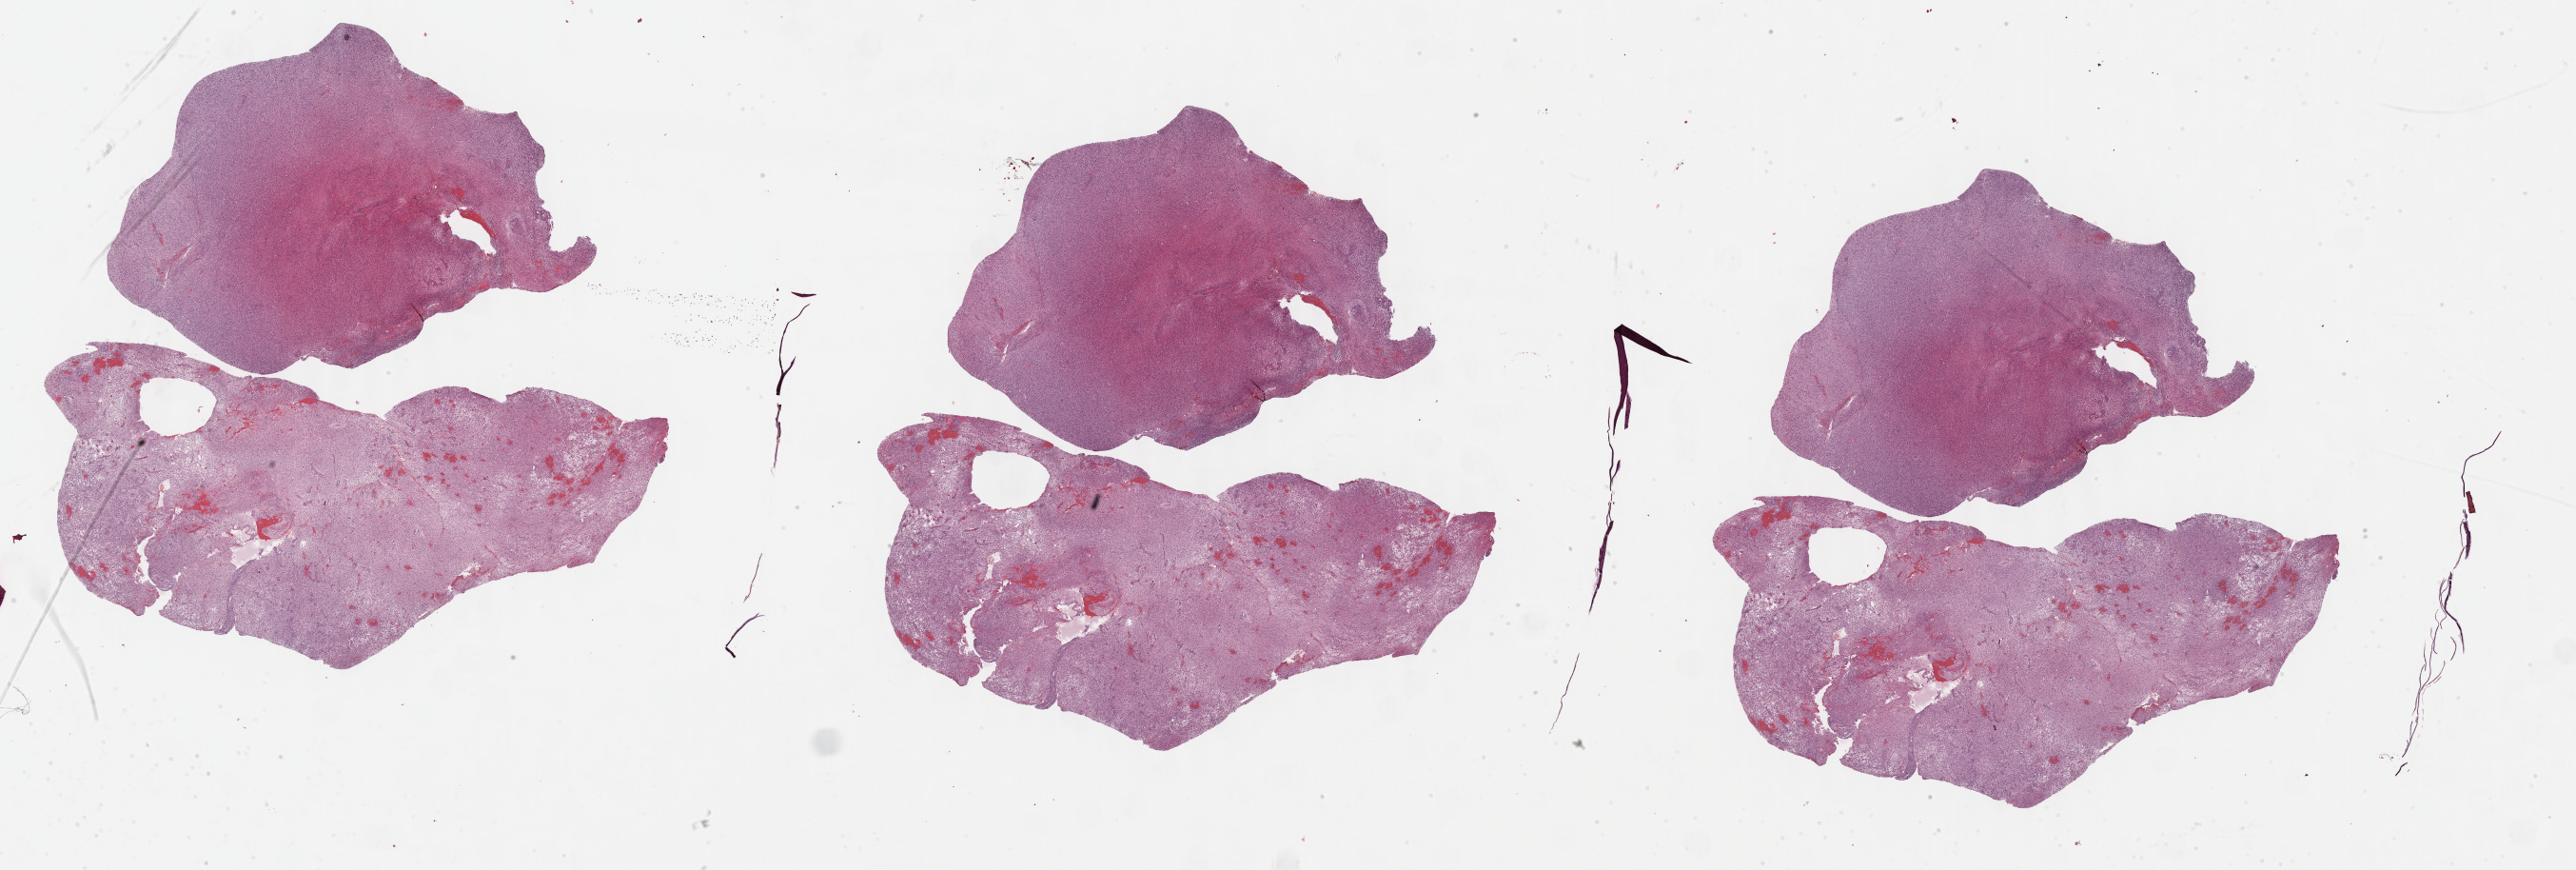
Whole-slide histology image, Hematoxylin and eosin (H&E) stained, low-resolution overview of the scanned area, about 43.8 x 14.8 mm (from a 40x scan); formalin-fixed paraffin-embedded (FFPE) diagnostic section; primary tumour sample from the brain. Female, age 54 years at initial diagnosis.
Diagnosis: Glioblastoma.